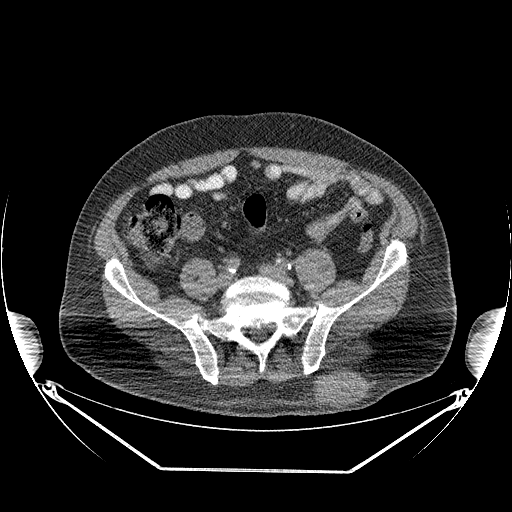
CT of an extremity soft-tissue mass (from a PET/CT study), one axial slice; slice 92 of 267 in the series (ordered by position); soft-tissue window (W 400 / L 40 HU); 3.75 mm slice thickness; 512 × 512 image matrix, field of view 500 × 500 mm. Male patient. Case-level facts recorded for this patient, not image findings: histological type: pleiomorphic leiomyosarcoma; grade: high; site of the primary tumour: left buttock.
Structures marked on this image (expert contour drawn on MRI and transferred to this co-registered scan by the dataset authors):
- gross tumour volume including surrounding oedema: bounding box (x1, y1, x2, y2) in pixels: (315, 370, 364, 408)
- gross tumour volume (mass): (315, 372, 364, 407)